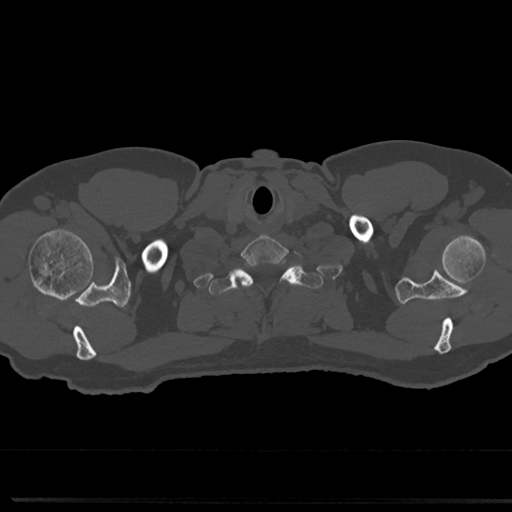
CT including the spine, one axial slice; slice 688 of 817 in the series (ordered by position); reconstruction kernel Br40s/3; 120 kVp; bone window (W 1800 / L 400 HU); 0.5 mm slice thickness; 512 × 512 image matrix. Male patient, age 61 years. From the clinical record (not read from this slice): primary cancer: prostate.
Annotated regions visible in this slice (semi-automatic segmentation, software-assisted and operator-edited):
- T1 vertebra: bounding box (x1, y1, x2, y2) in pixels: (212, 261, 317, 344)